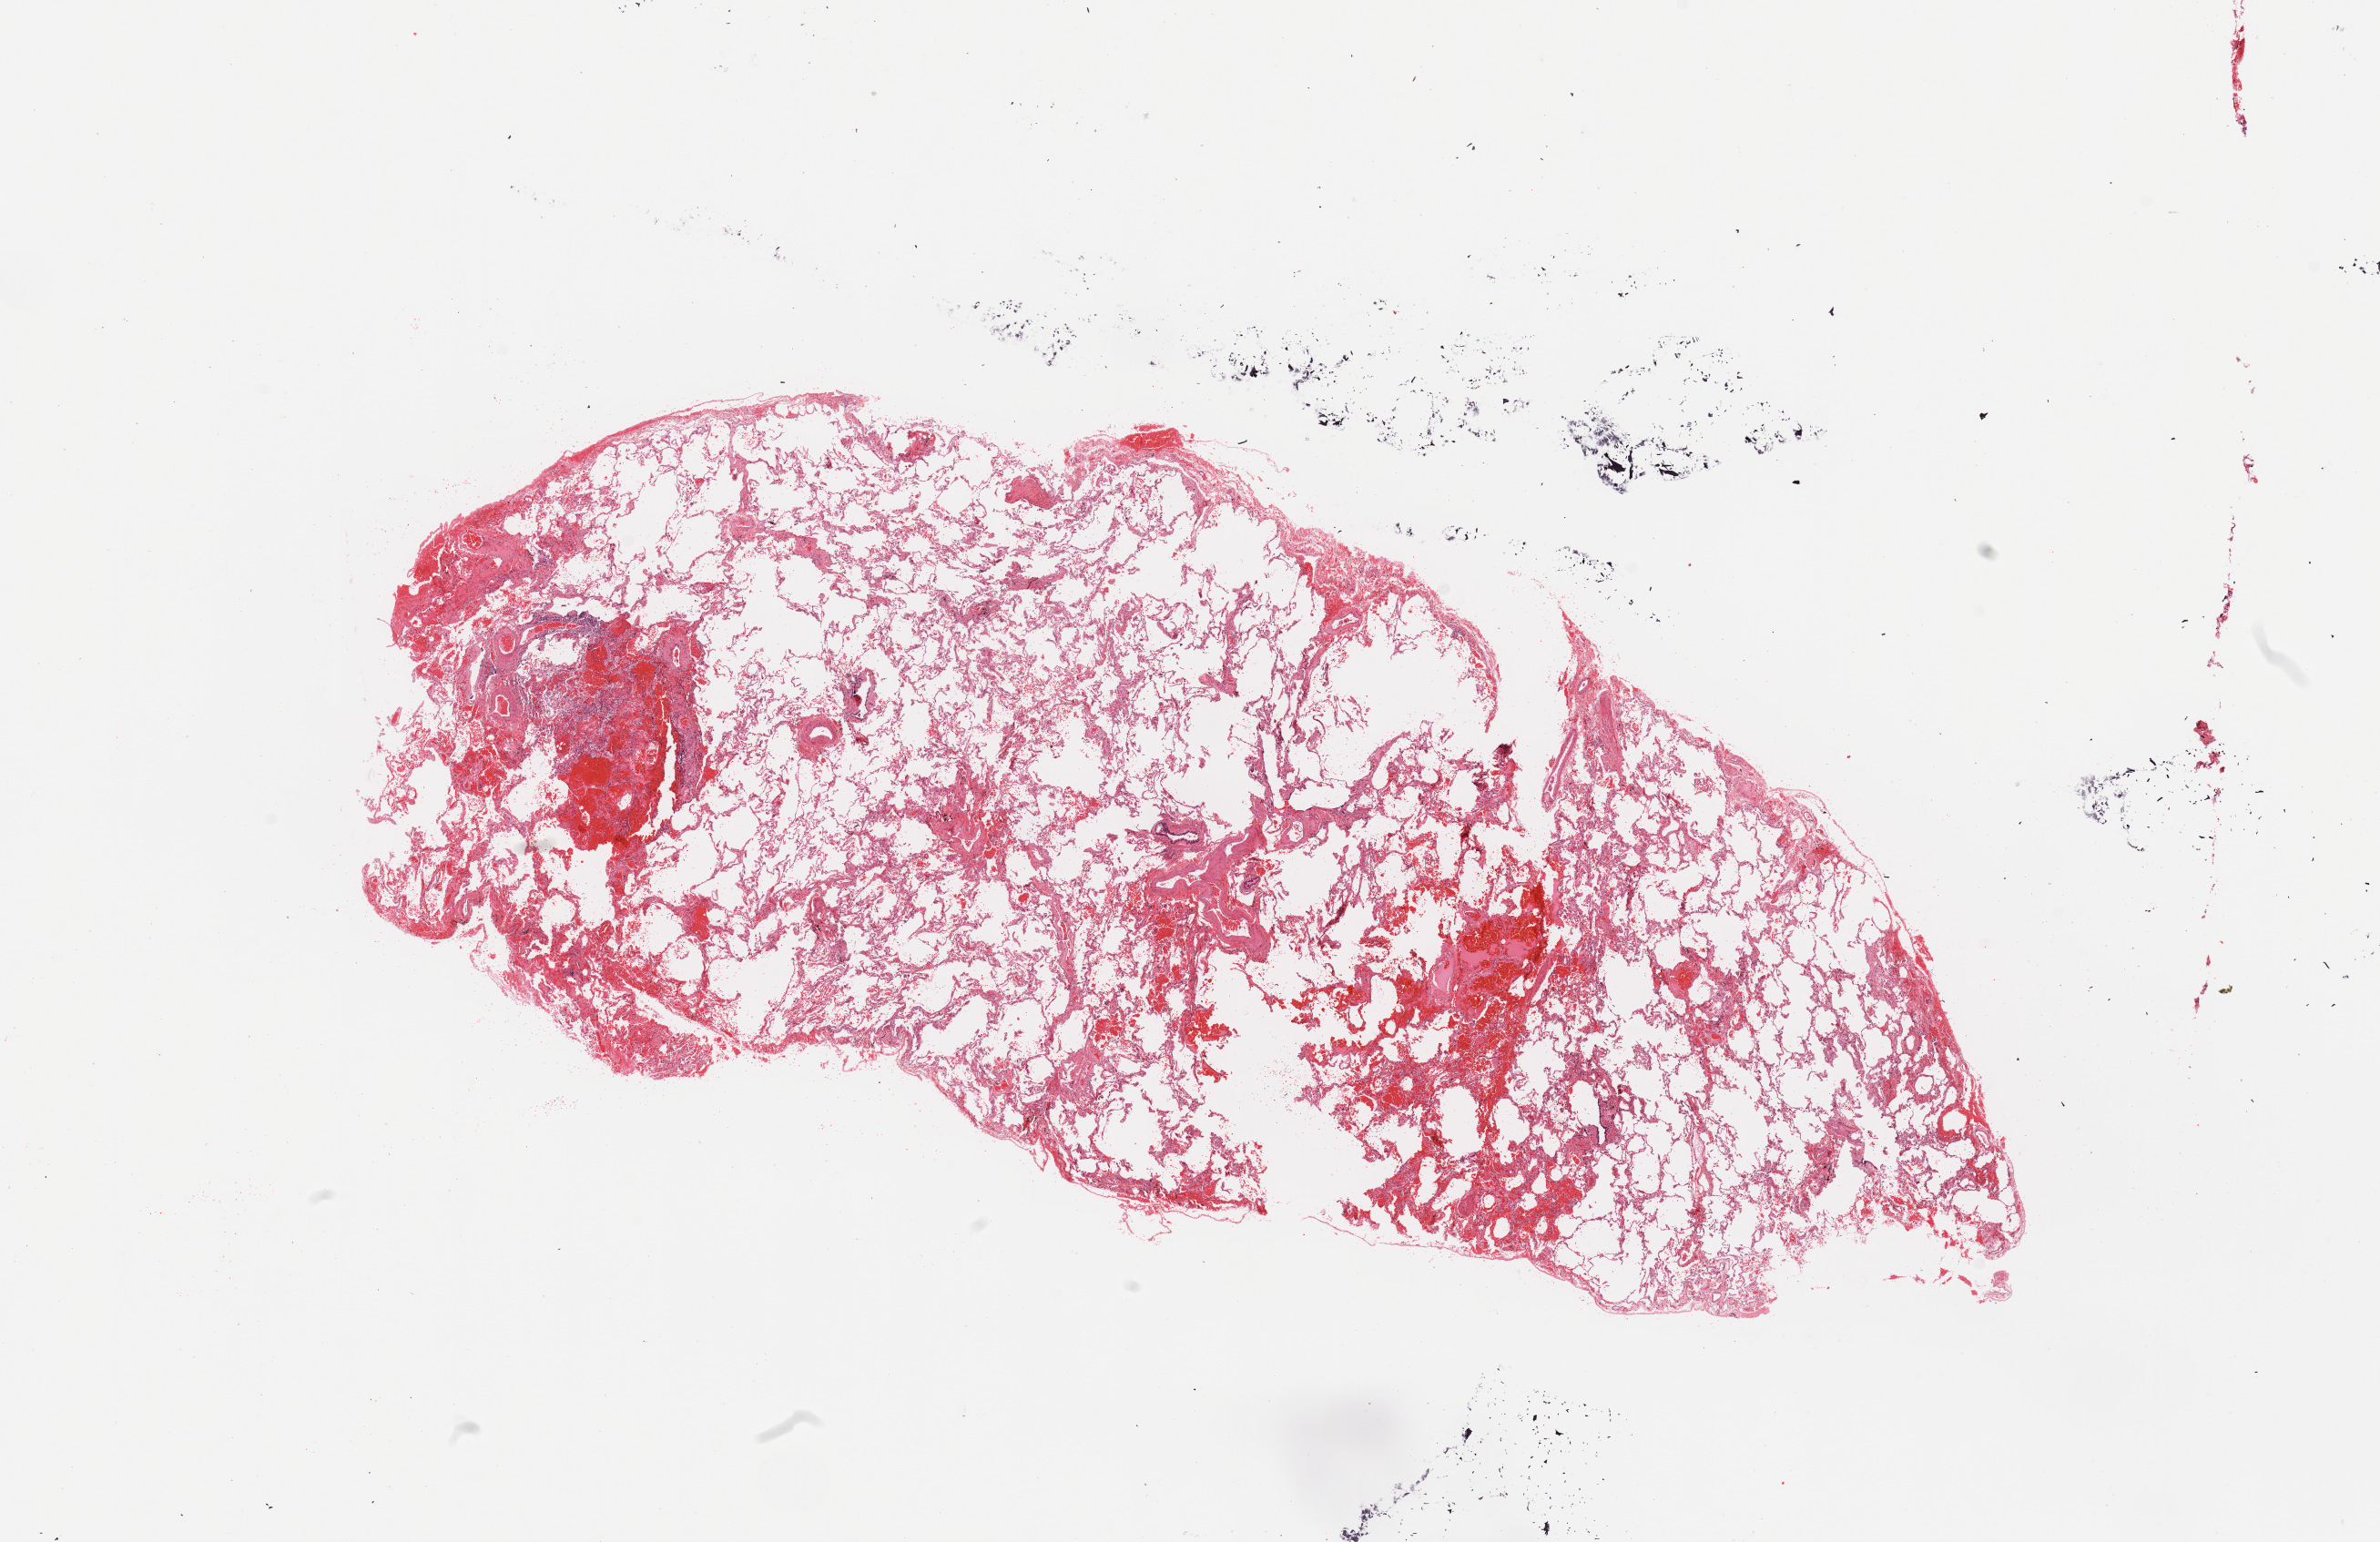
H&E whole-slide image, low-resolution overview of the scanned area, about 20.7 x 13.4 mm (acquisition: 20x scan); normal (non-tumour) tissue sample, sampled site: lung. 68-year-old female patient.
This section: normal (non-tumour) tissue from the same patient. Patient diagnosis: Adenocarcinoma, NOS.